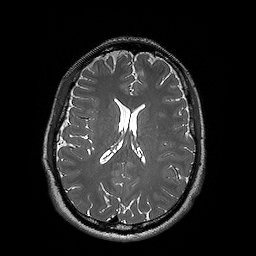
Brain MRI from a brain-tumour surgery series, one axial slice; position 74 of 192 along the scan axis; 1 mm slice thickness; 256 × 256 image matrix, field of view 250 × 250 mm. Case-level facts recorded for this patient, not image findings: histopathology: Oligodendroglioma; WHO grade: 2; IDH mutation: yes; tumour location: Left Posterior Temporal.
Annotated regions visible in this slice (expert manual segmentation):
- tumour: bounding box [x1, y1, x2, y2] px = [164, 168, 177, 180]